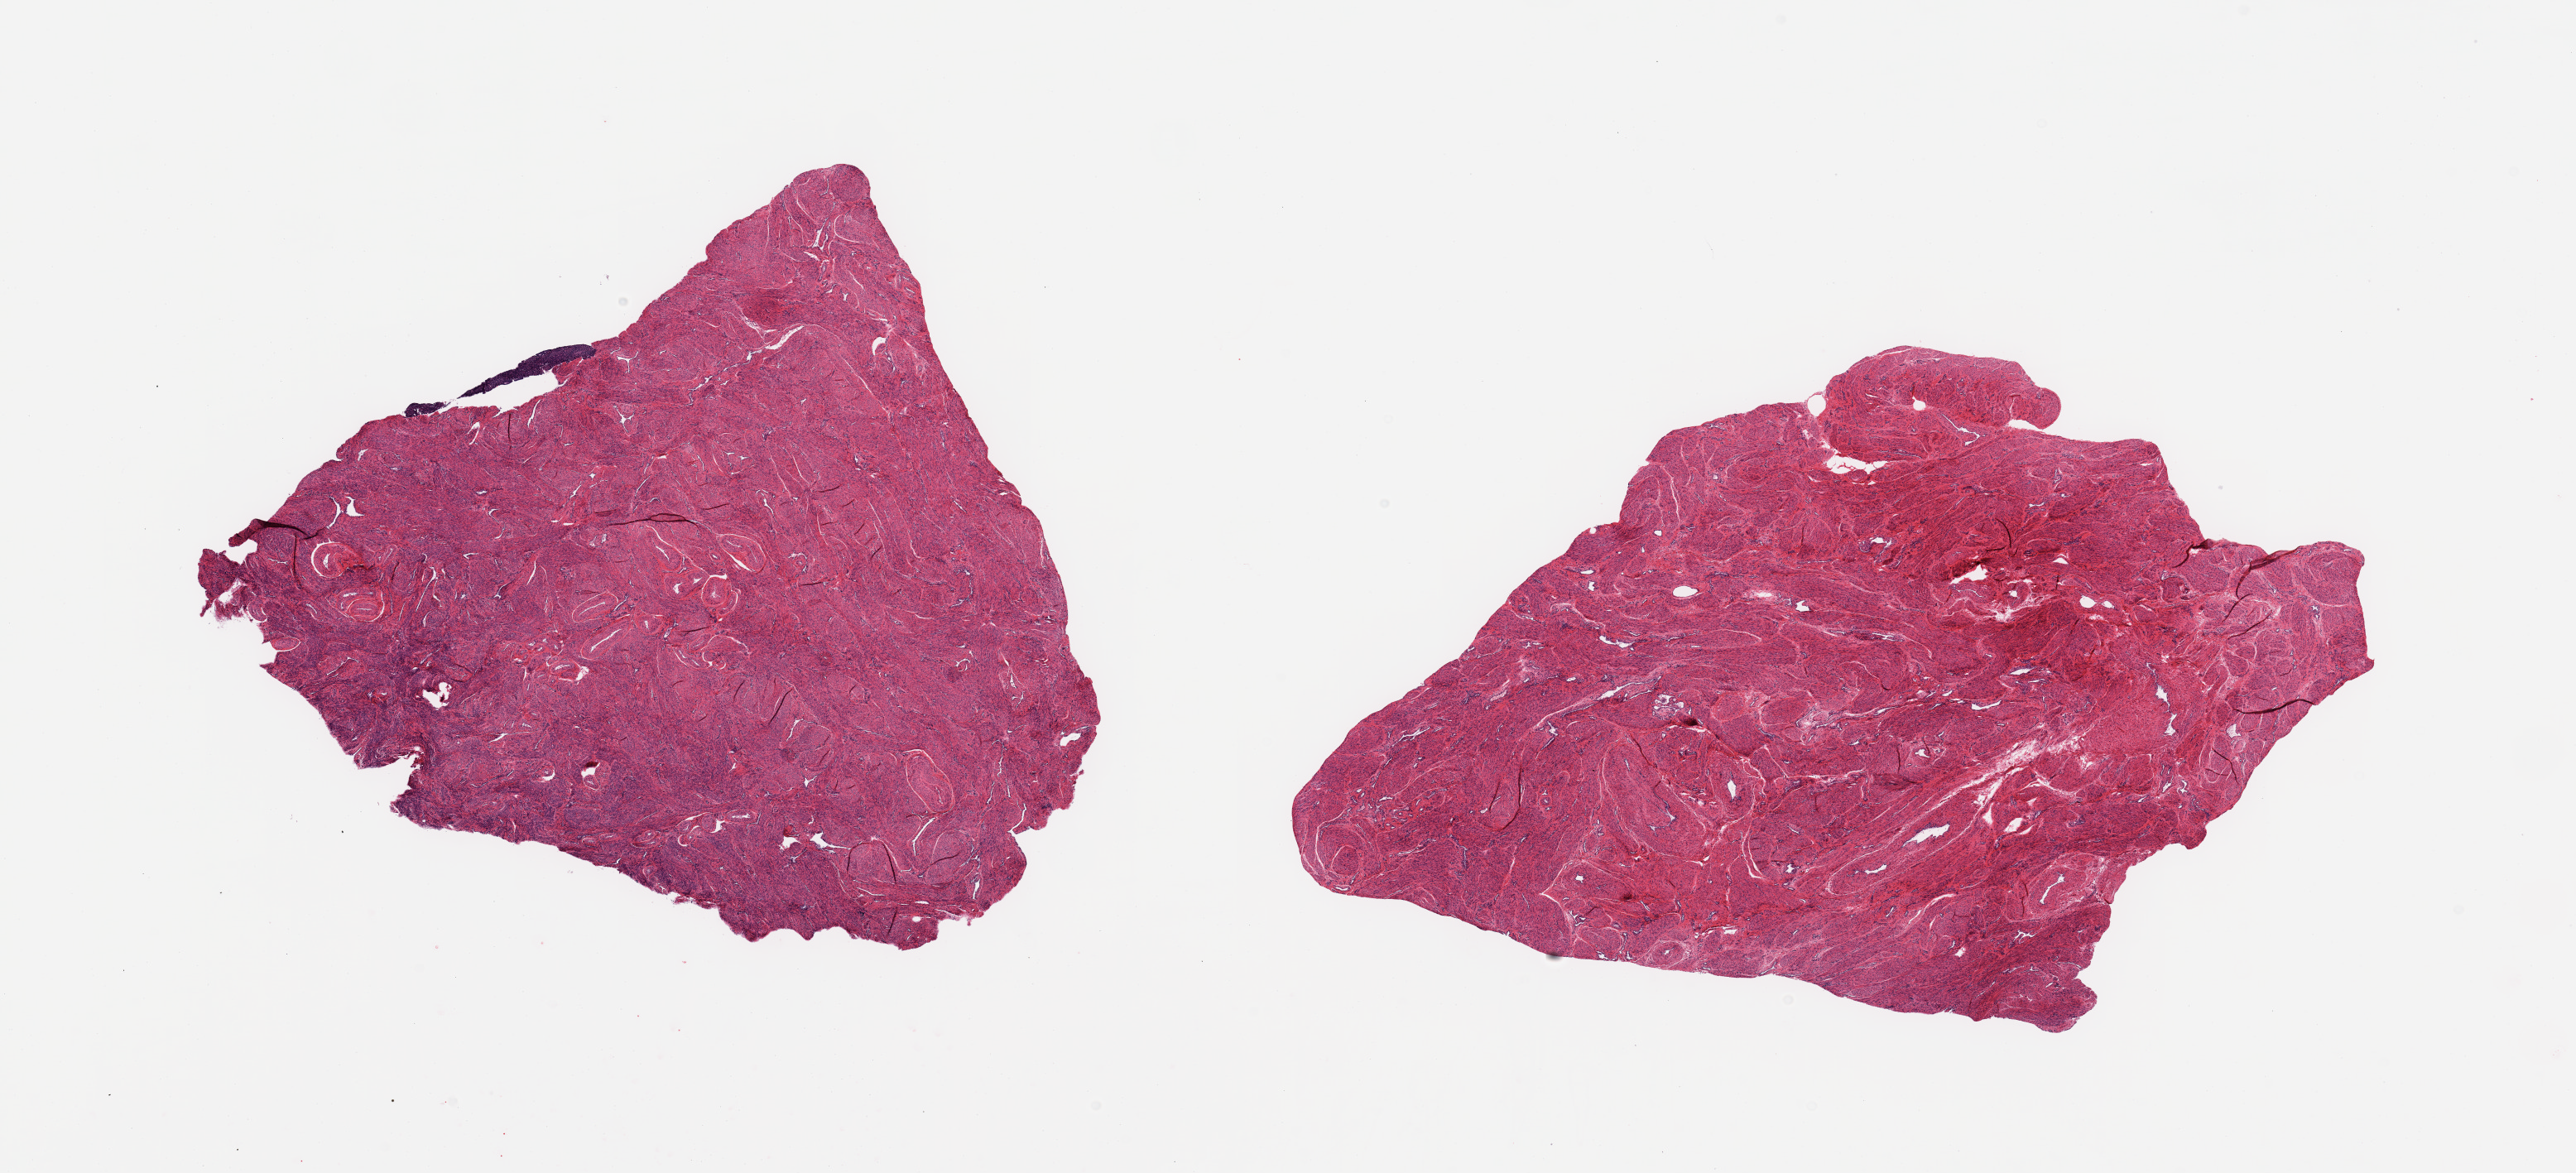
Hematoxylin and eosin (H&E) whole-slide image — low-resolution overview of the scanned area, about 24.6 x 11.2 mm (acquisition: 20x scan). PAXgene-fixed paraffin-embedded (PFPE) section. Target tissue: uterus. Donor tissue sample. Donor: female.
Review note (as recorded): 2 pieces; all myometrium except for 1 small focus of proliferative endometrium.